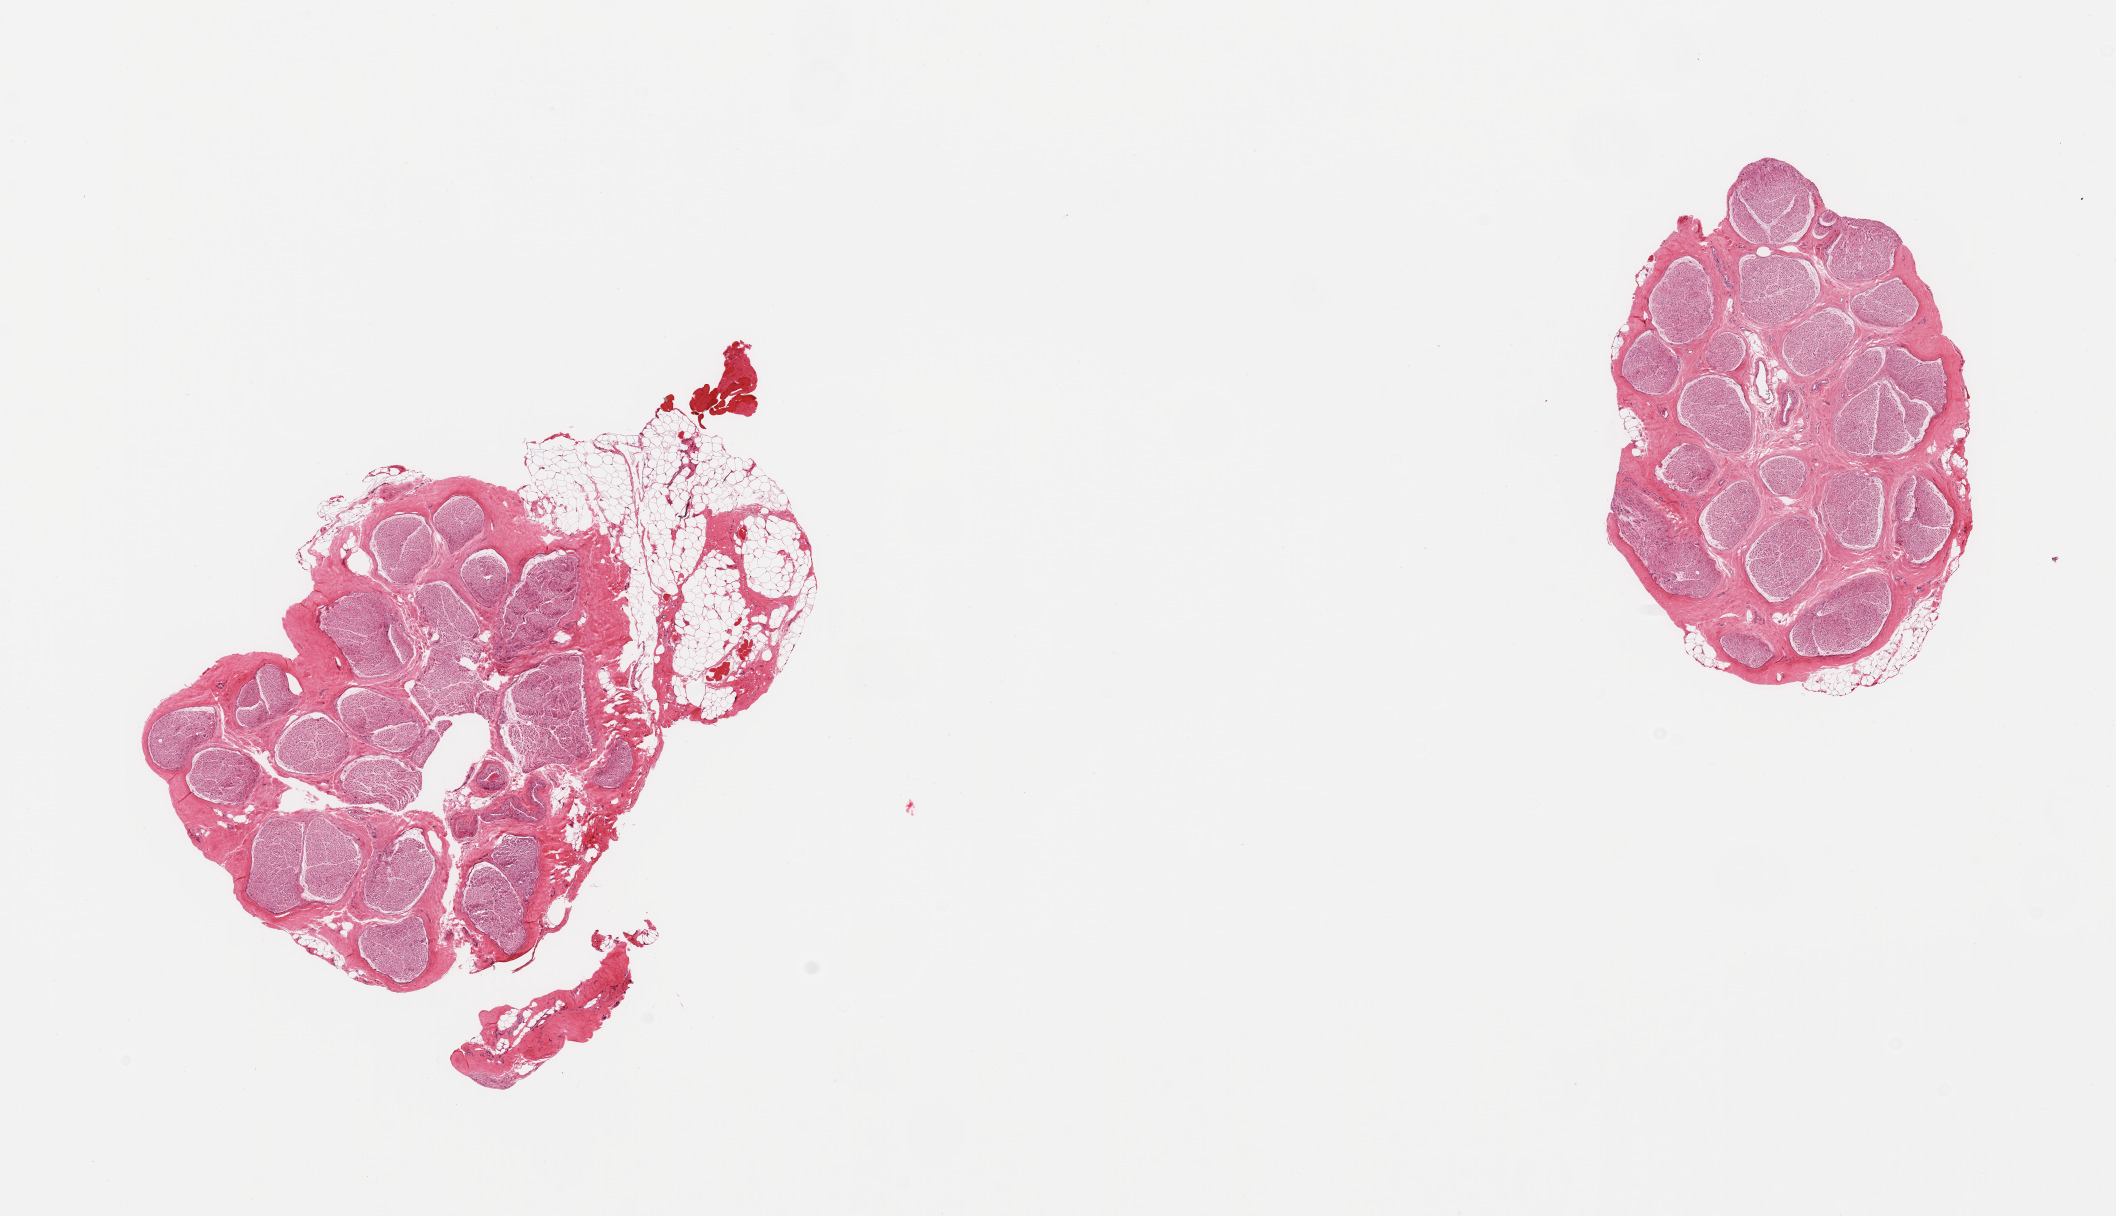
Whole-slide image, hematoxylin and eosin (H&E) stain — a low-resolution overview of the entire scanned area, about 16.7 x 9.6 mm (slide scanned at 20x), PAXgene-fixed paraffin-embedded (PFPE) section, section of tibial nerve (target tissue), tissue donor sample.
- reviewer comment on this tissue sample: 2 pieces; includes from 5-25% attached fat/skeletal muscle